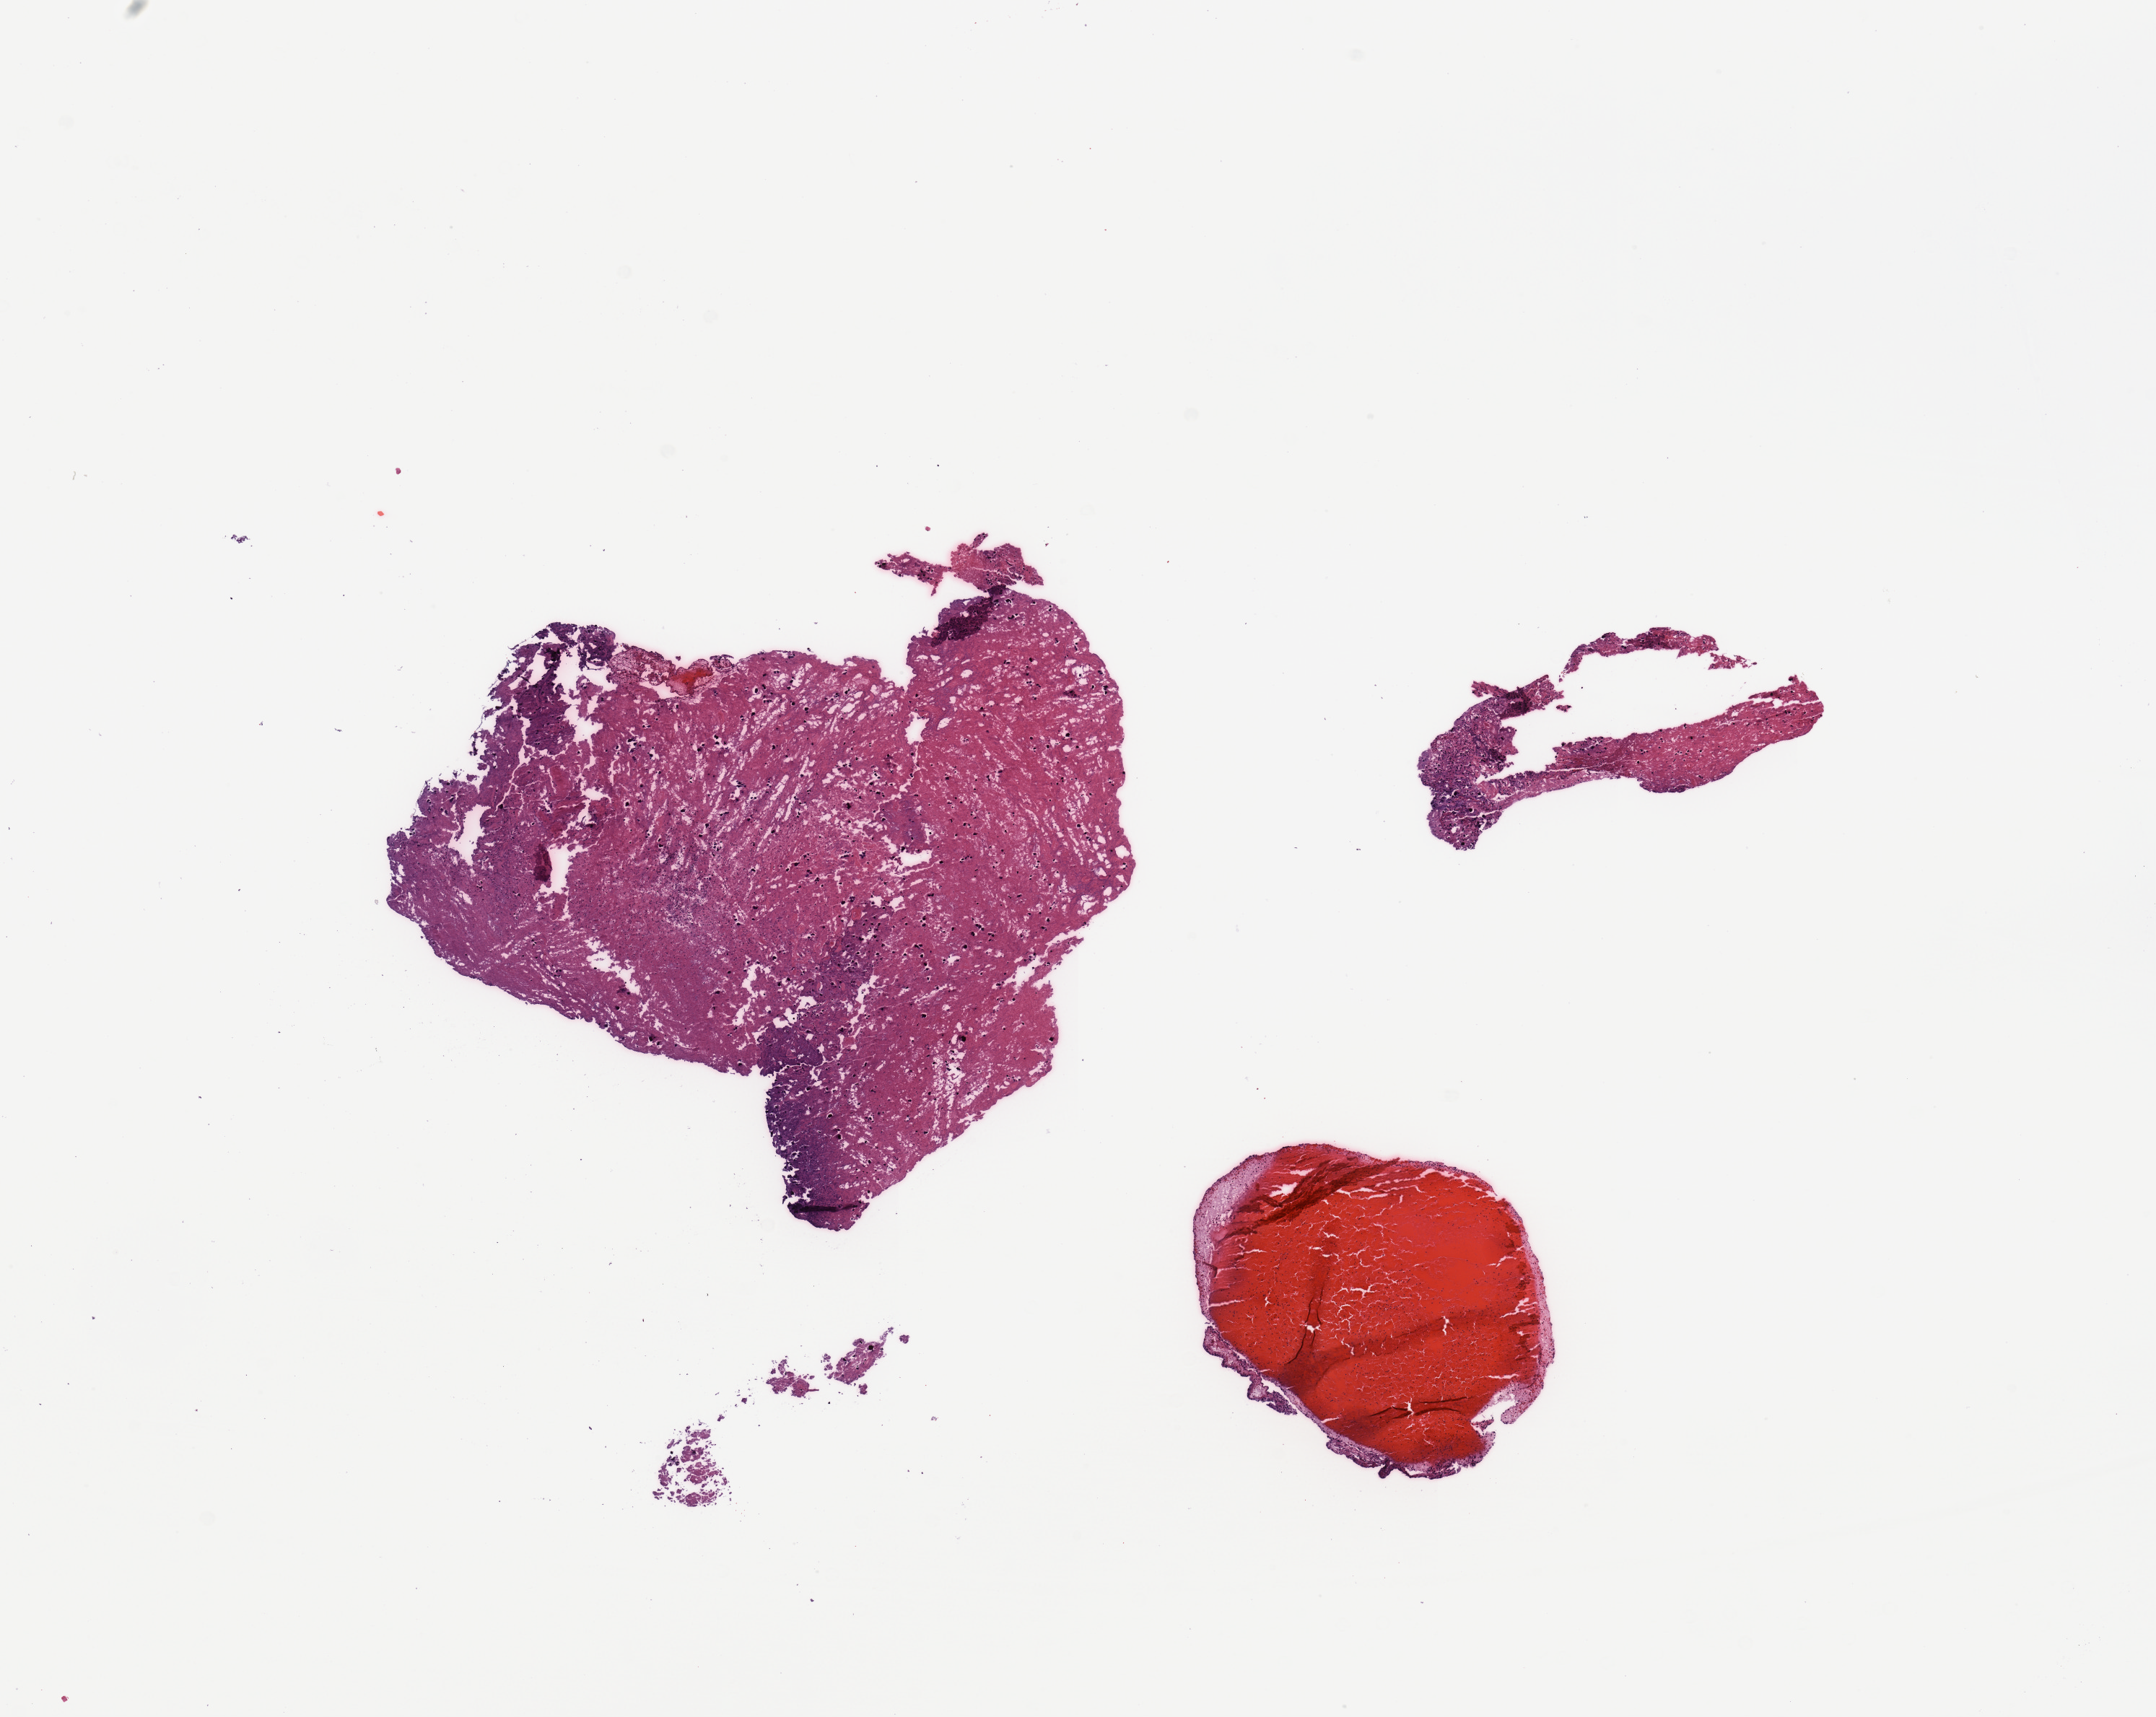
Hematoxylin and eosin (H&E) stained whole-slide image, shown as a low-resolution overview of the whole scanned area (about 11.8 x 9.4 mm); tumour tissue sample, brain. Female, 59 y/o.
Primary tumour site (as recorded): frontal lobe. Histologic diagnosis: Glioblastoma.